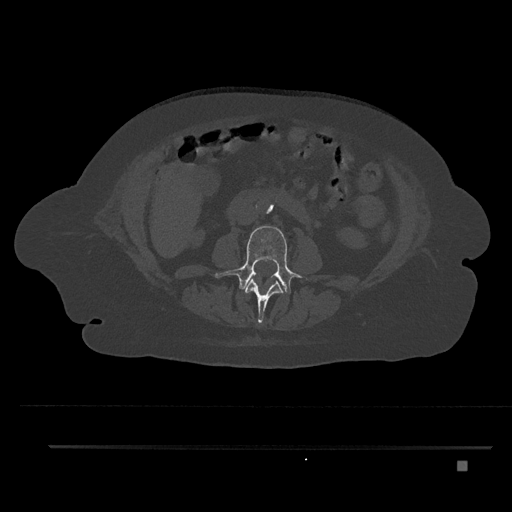
CT including the spine, one axial slice. Slice 142 of 797 in the series (ordered by position). Bone window (W 1800 / L 400 HU). 0.5 mm slice thickness. 512 × 512 image matrix, field of view 437 × 437 mm. Female patient, age 76 years. Case-level facts recorded for this patient, not image findings: primary cancer: lung; vertebrae with lytic lesions (as recorded): T11, L3.
Annotated regions visible in this slice (semi-automatic segmentation, software-assisted and operator-edited):
- L2 vertebra: bounding box [x1, y1, x2, y2] px = [245, 278, 284, 324]
- L3 vertebra: [215, 225, 300, 294]